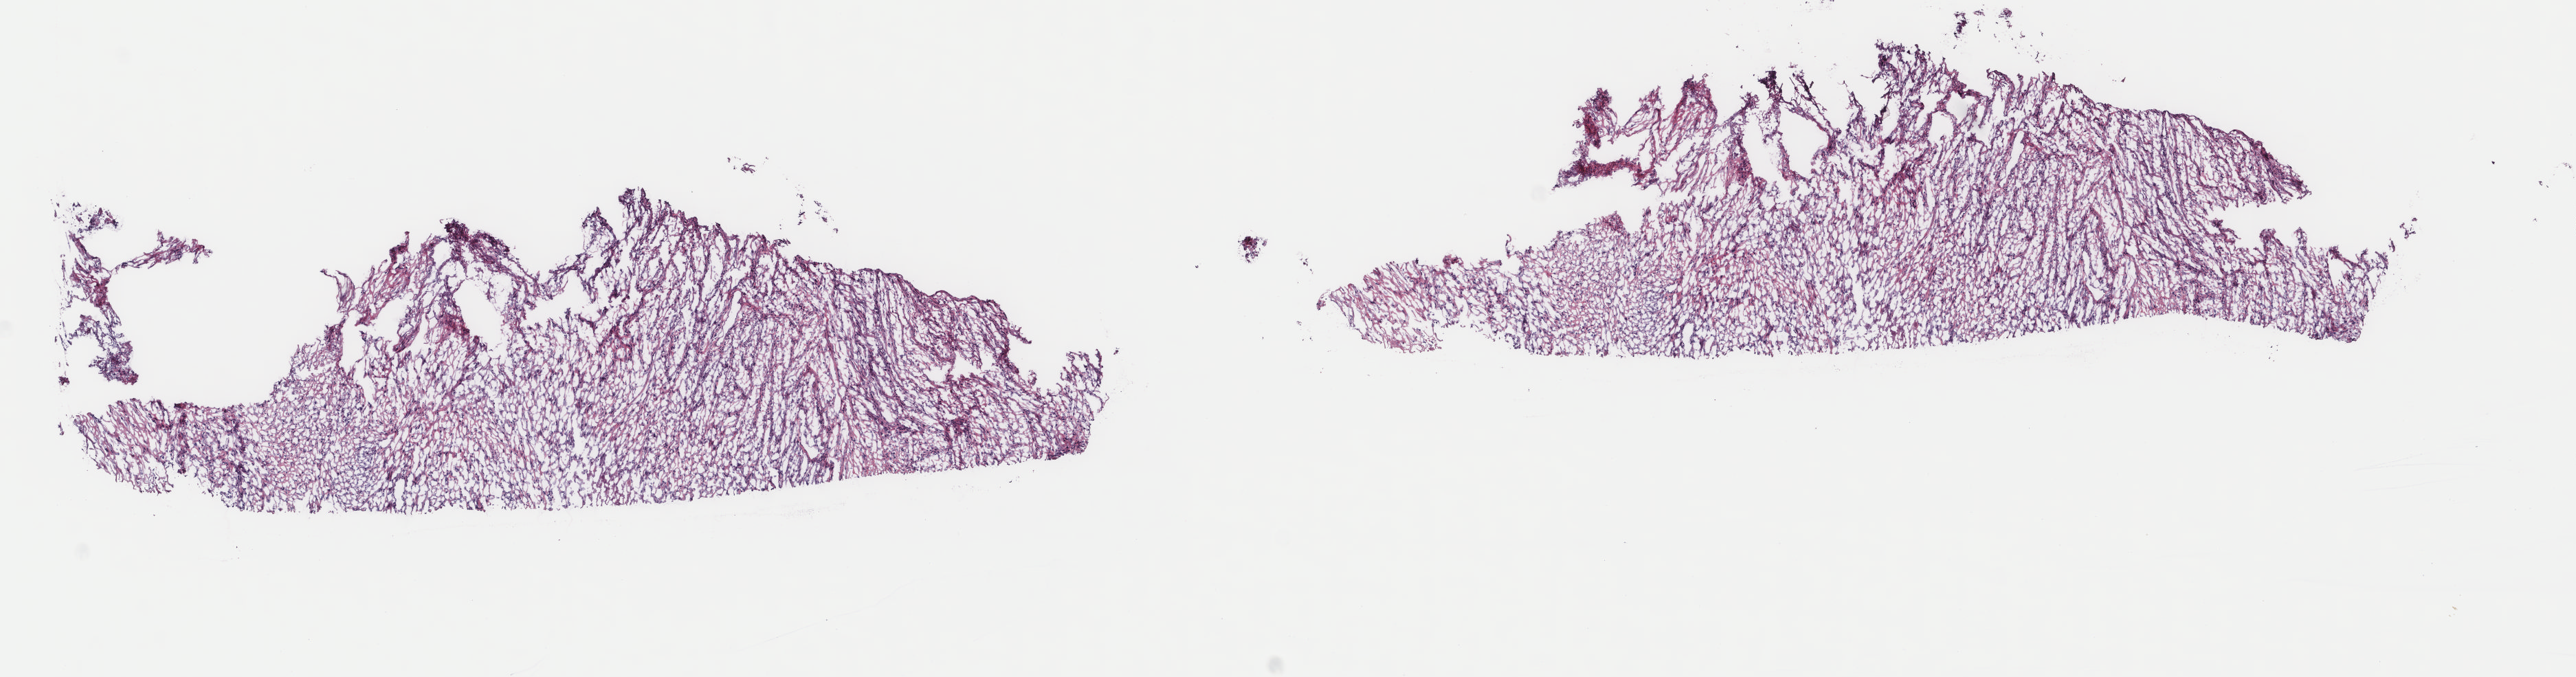
H&E-stained whole-slide image, shown as a low-resolution overview of the whole scanned area (about 14.9 x 3.9 mm, slide scanned at 40x), frozen section, connective, subcutaneous and other soft tissues, primary tumour sample. Male, age 80 years at initial diagnosis.
Pathologic diagnosis: Liposarcoma, NOS (connective, subcutaneous and other soft tissues, NOS).